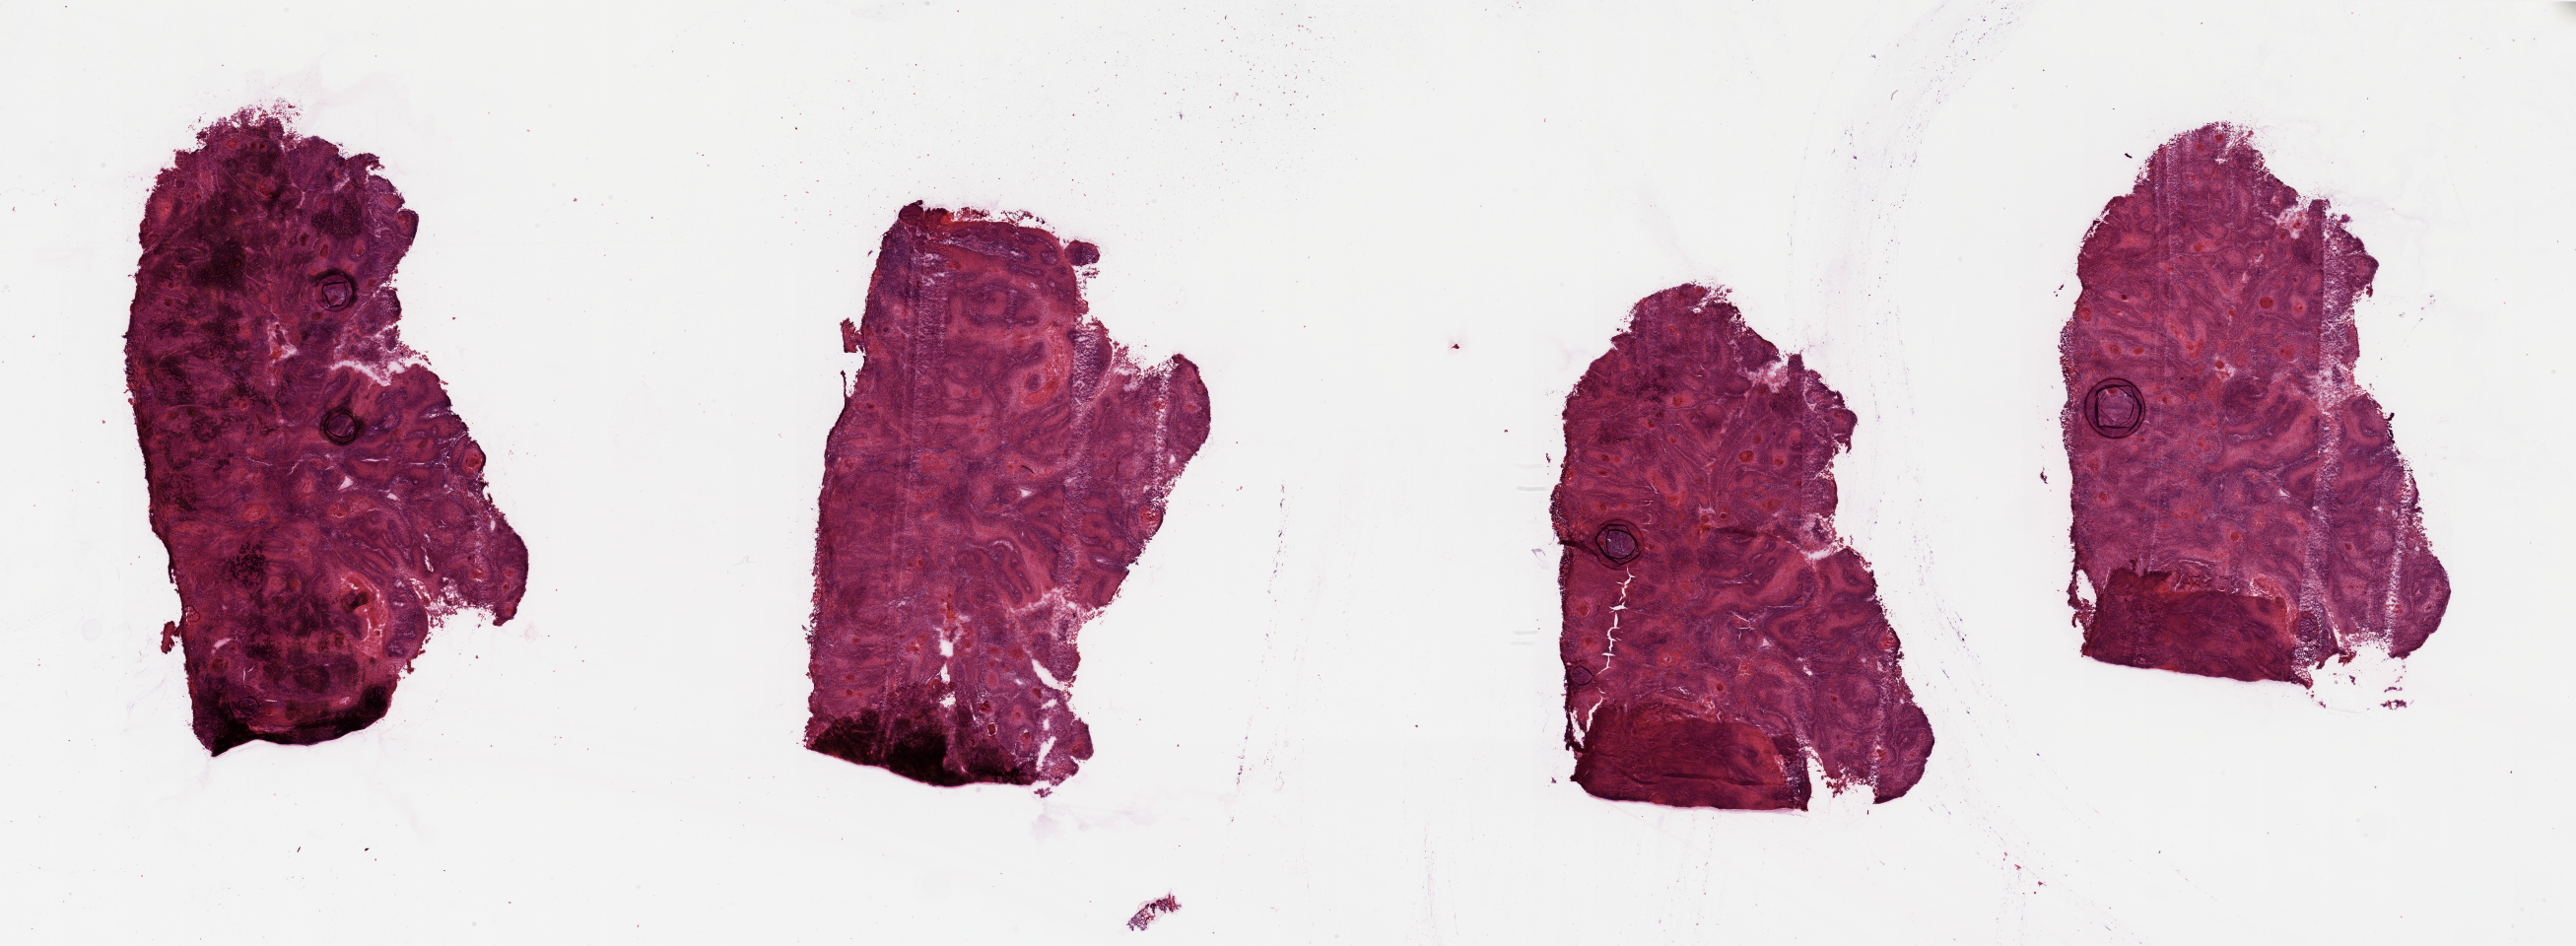
Digitized H&E tissue section (whole slide), whole scanned area (about 41.3 x 15.2 mm, from a 20x scan) shown as a low-resolution overview, head and neck, tissue type not recorded. Male, 54 y/o.
• patient diagnosis: Squamous cell carcinoma, NOS (lip, NOS)